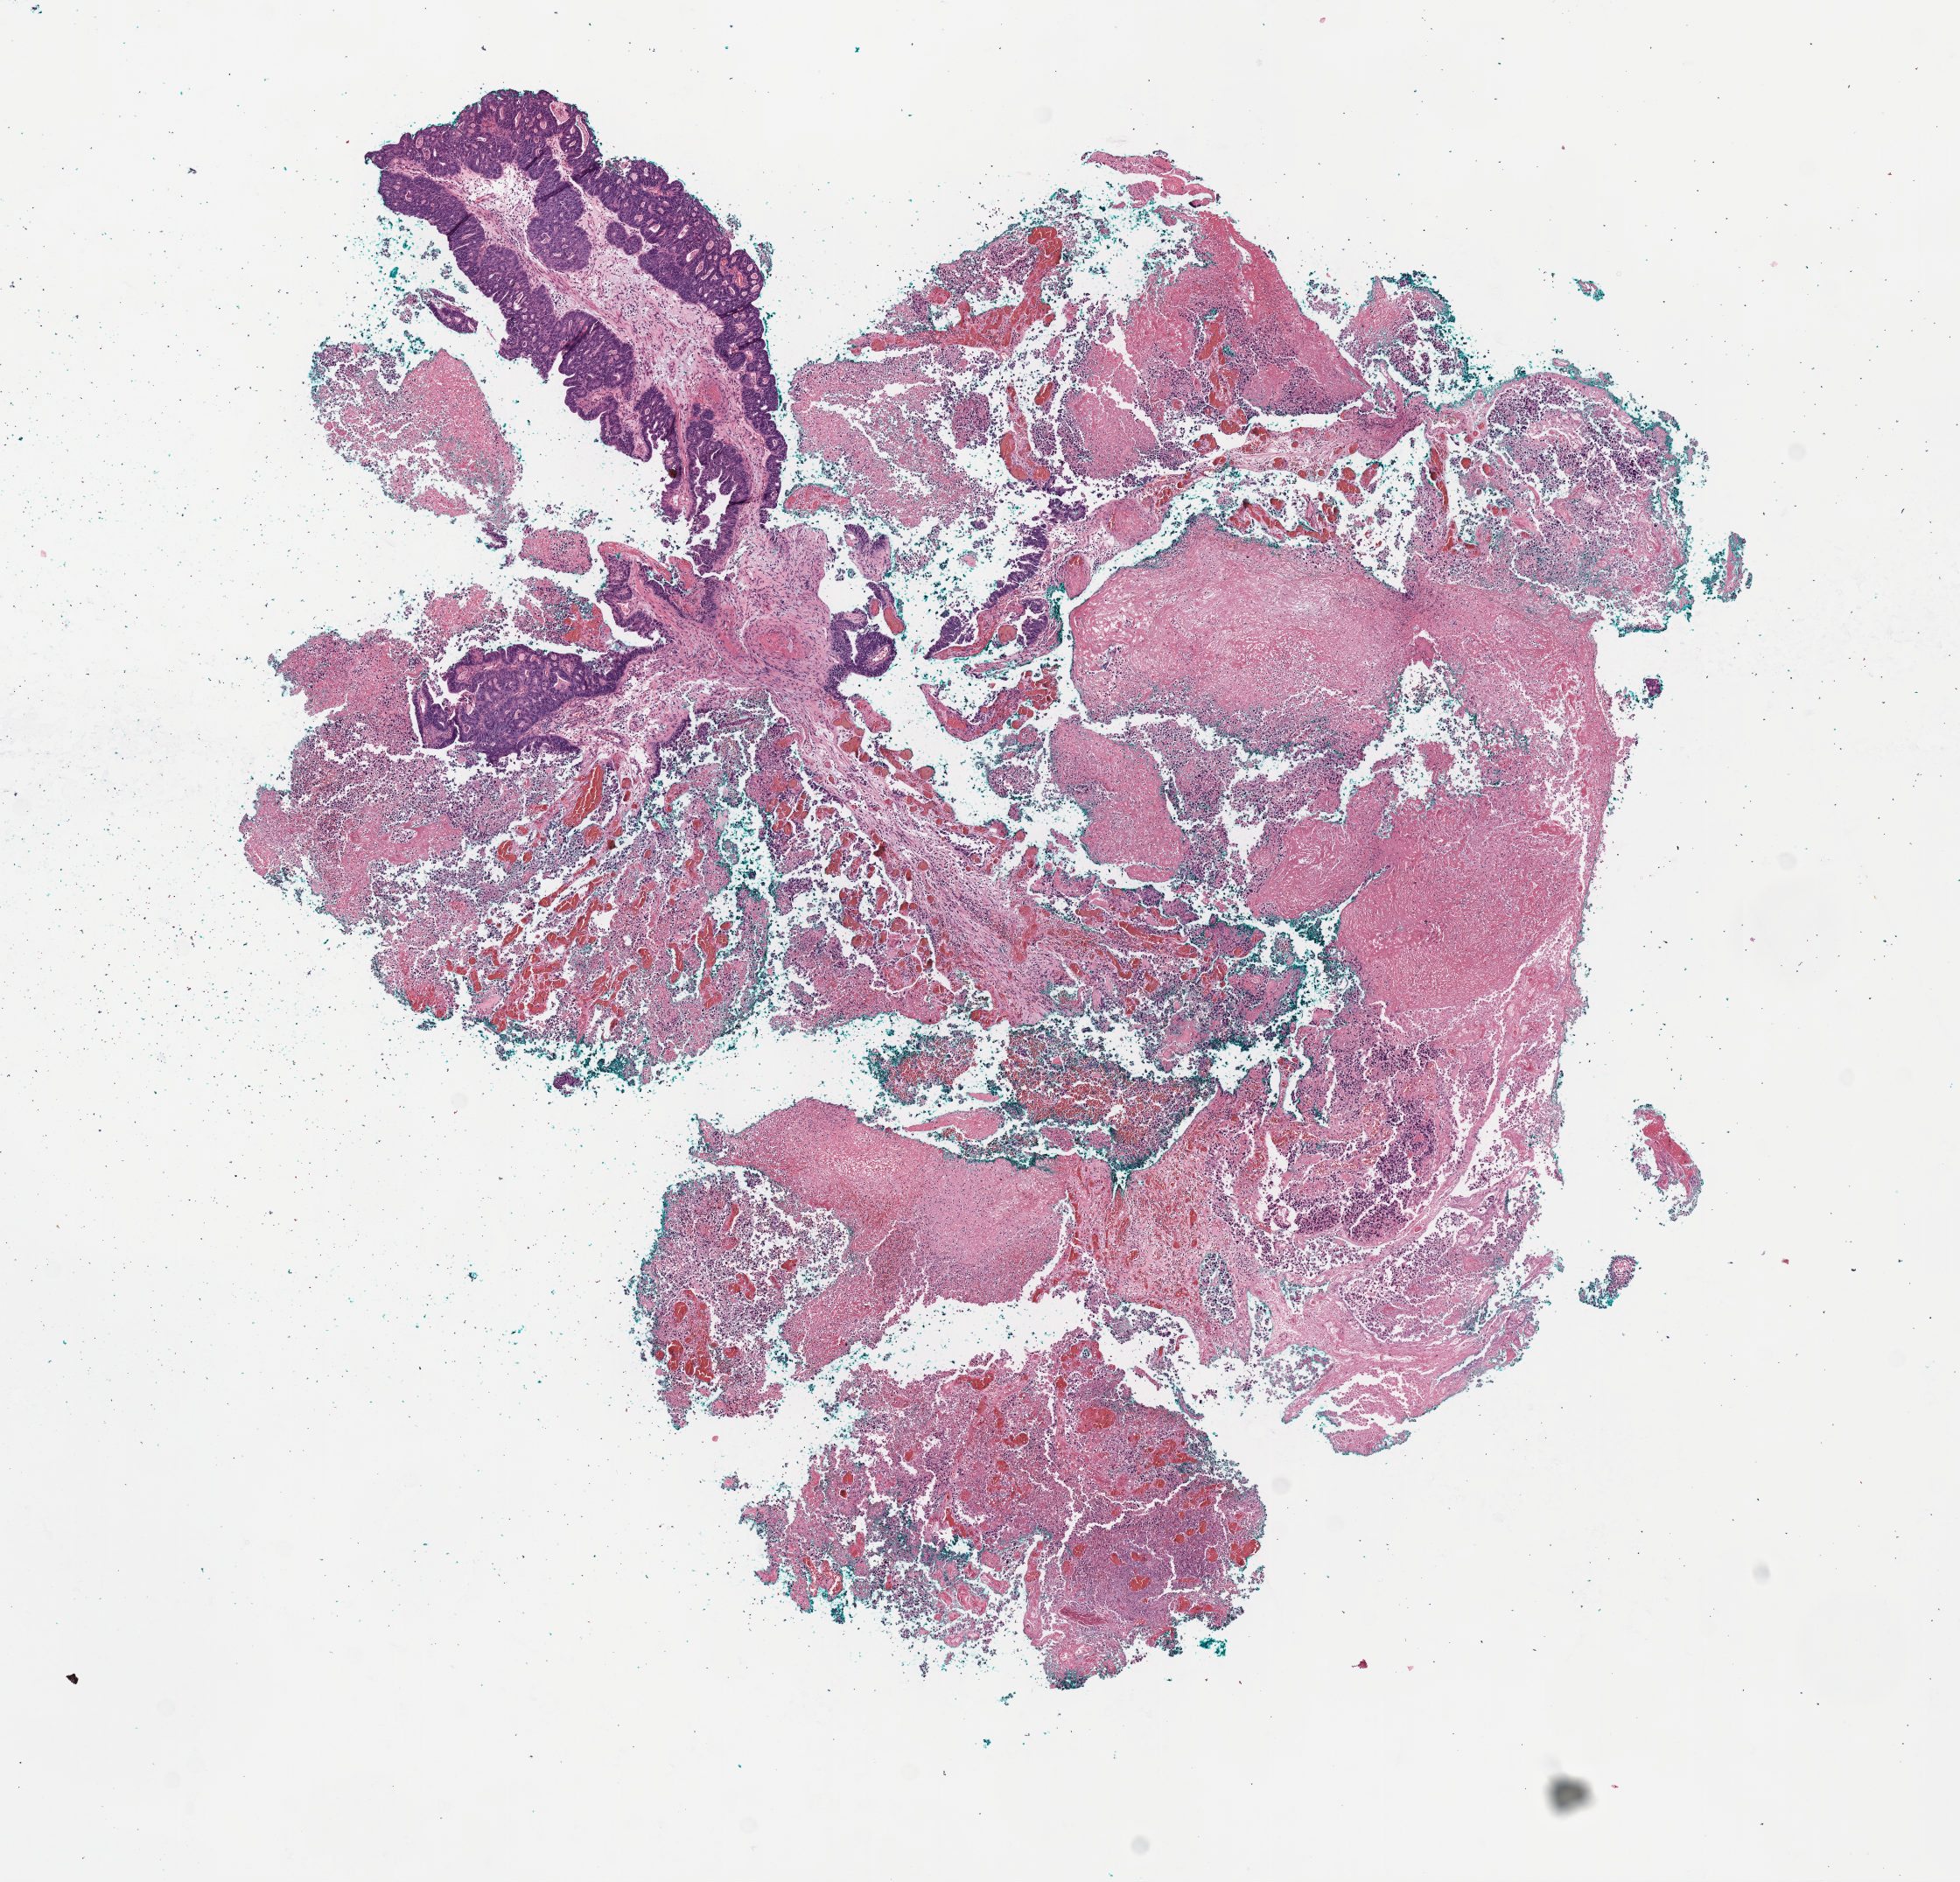
Digitized H&E-stained tissue section (whole slide), shown as a low-resolution overview of the whole scanned area (about 9.1 x 8.7 mm, from a 40x scan); FFPE section; primary tumour sample from the cervix. Patient: female, age at initial diagnosis 63 years. Histologic grade: G2 (moderately differentiated).
Pathologic diagnosis: Mucinous adenocarcinoma, endocervical type (cervix uteri). FIGO stage: IVA.